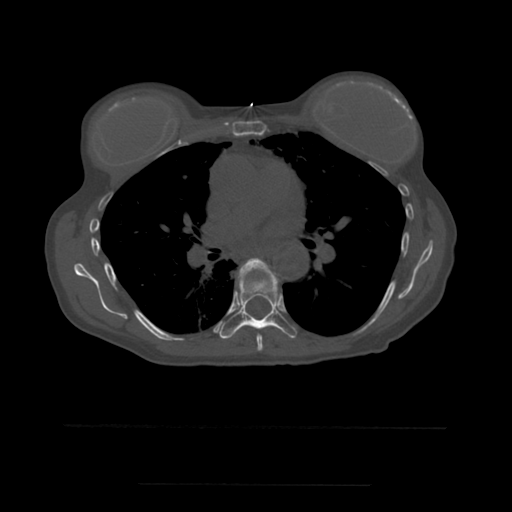
CT including the spine, one axial slice; position 363 of 544 along the scan axis; bone window (W 1800 / L 400 HU); 1.25 mm slice thickness; 512 × 512 image matrix, field of view 350 × 350 mm. Patient age 58 years. Case-level facts recorded for this patient, not image findings: primary cancer: lung.
Annotated regions visible in this slice (semi-automatically segmented with operator editing):
- T6 vertebra: bounding box <240,258,273,351> (left, top, right, bottom; pixels)
- T7 vertebra: <215,258,297,339>